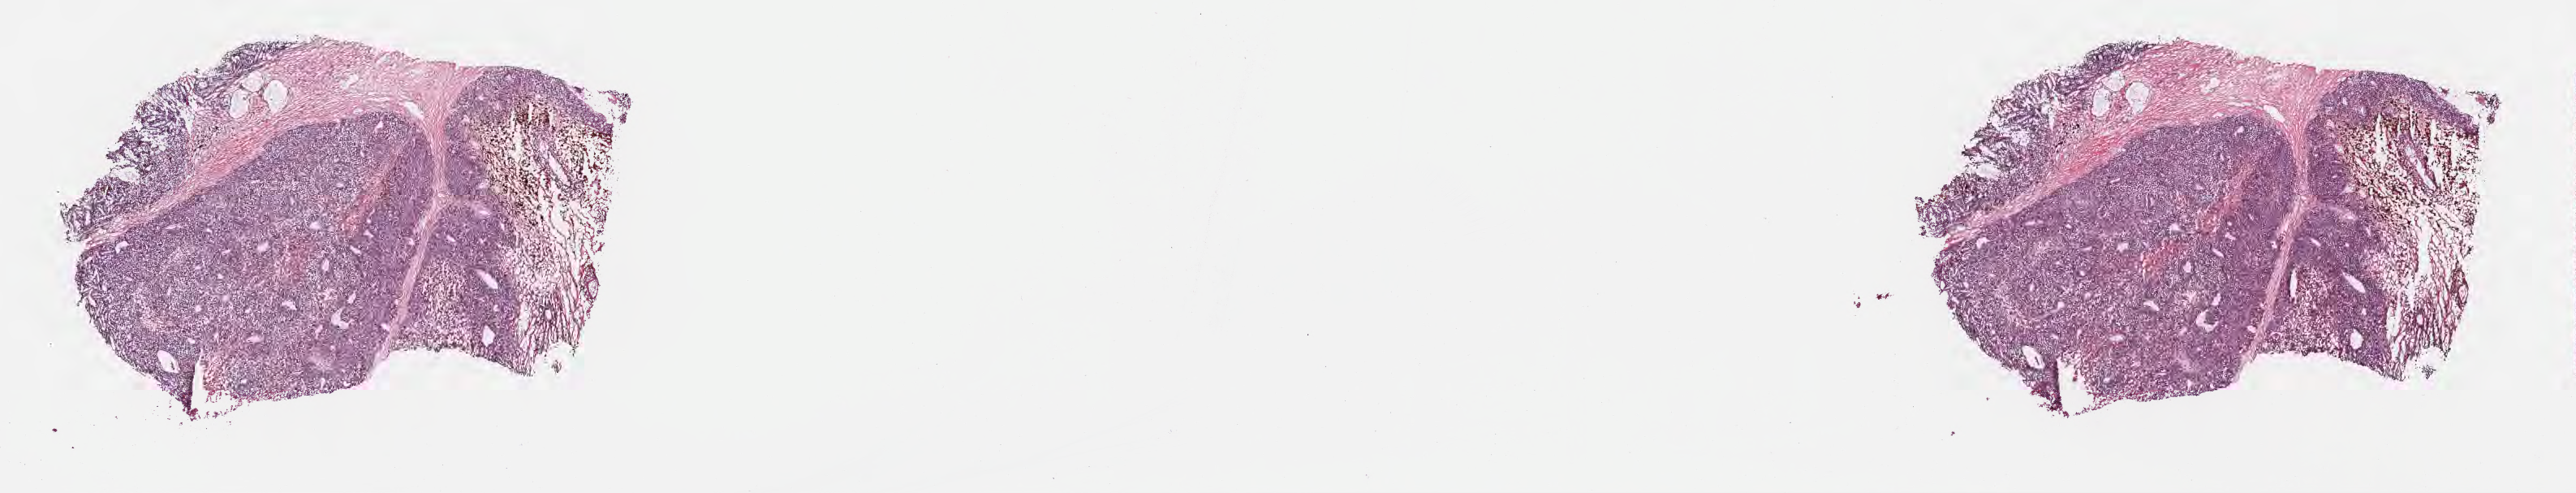
Digitized haematoxylin and eosin-stained section, low-resolution overview of the scanned area, about 25.7 x 4.9 mm, frozen section, metastatic tumor tissue, resected from lymph nodes of axilla or arm. Male, age 63 years at initial diagnosis. Composition of this section per pathologist review: tumor cells 70%, tumor nuclei 85%, stromal cells 0%, necrosis 15%, normal cells 15%. Inflammatory infiltration, as recorded: lymphocyte infiltration 0%, monocyte infiltration 0%, neutrophil infiltration 0%.
Section: bottom of the tissue portion. Patient diagnosis (primary): Malignant melanoma, NOS.